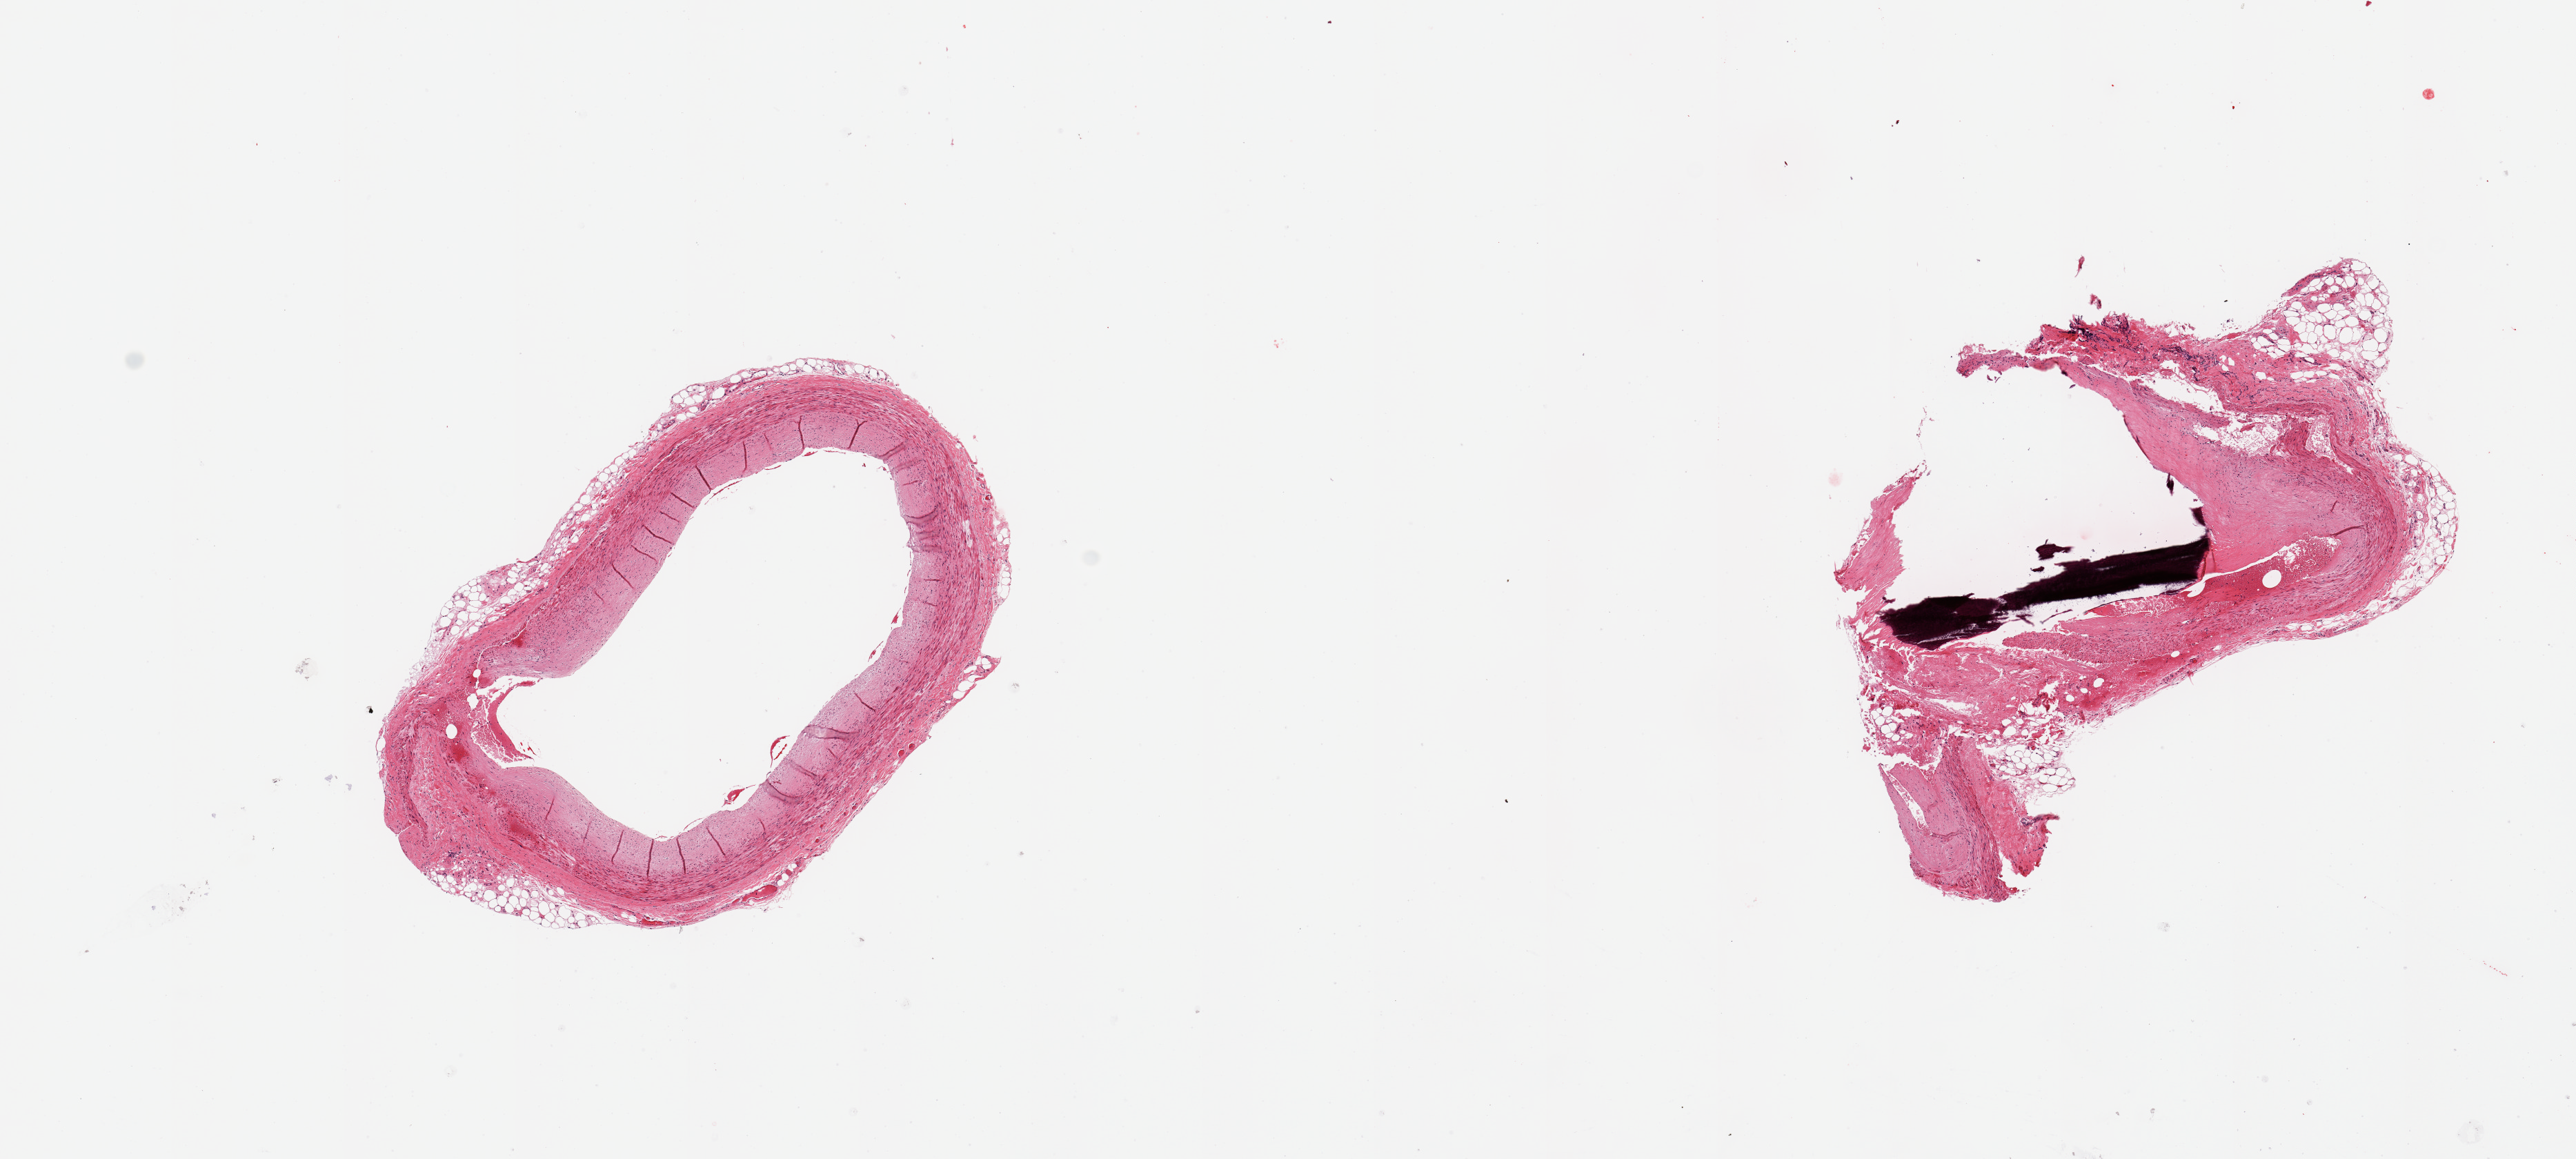
Haematoxylin and eosin whole-slide image, shown as a low-resolution overview of the whole scanned area (about 14.8 x 6.6 mm, acquisition: 20x scan). PAXgene-fixed, paraffin-embedded tissue. Sampled site (target tissue): coronary artery. Donor tissue sample. Donor: male.
Review note (as recorded): 2 pieces, subtotally occlusive and focally calcified atherosis.